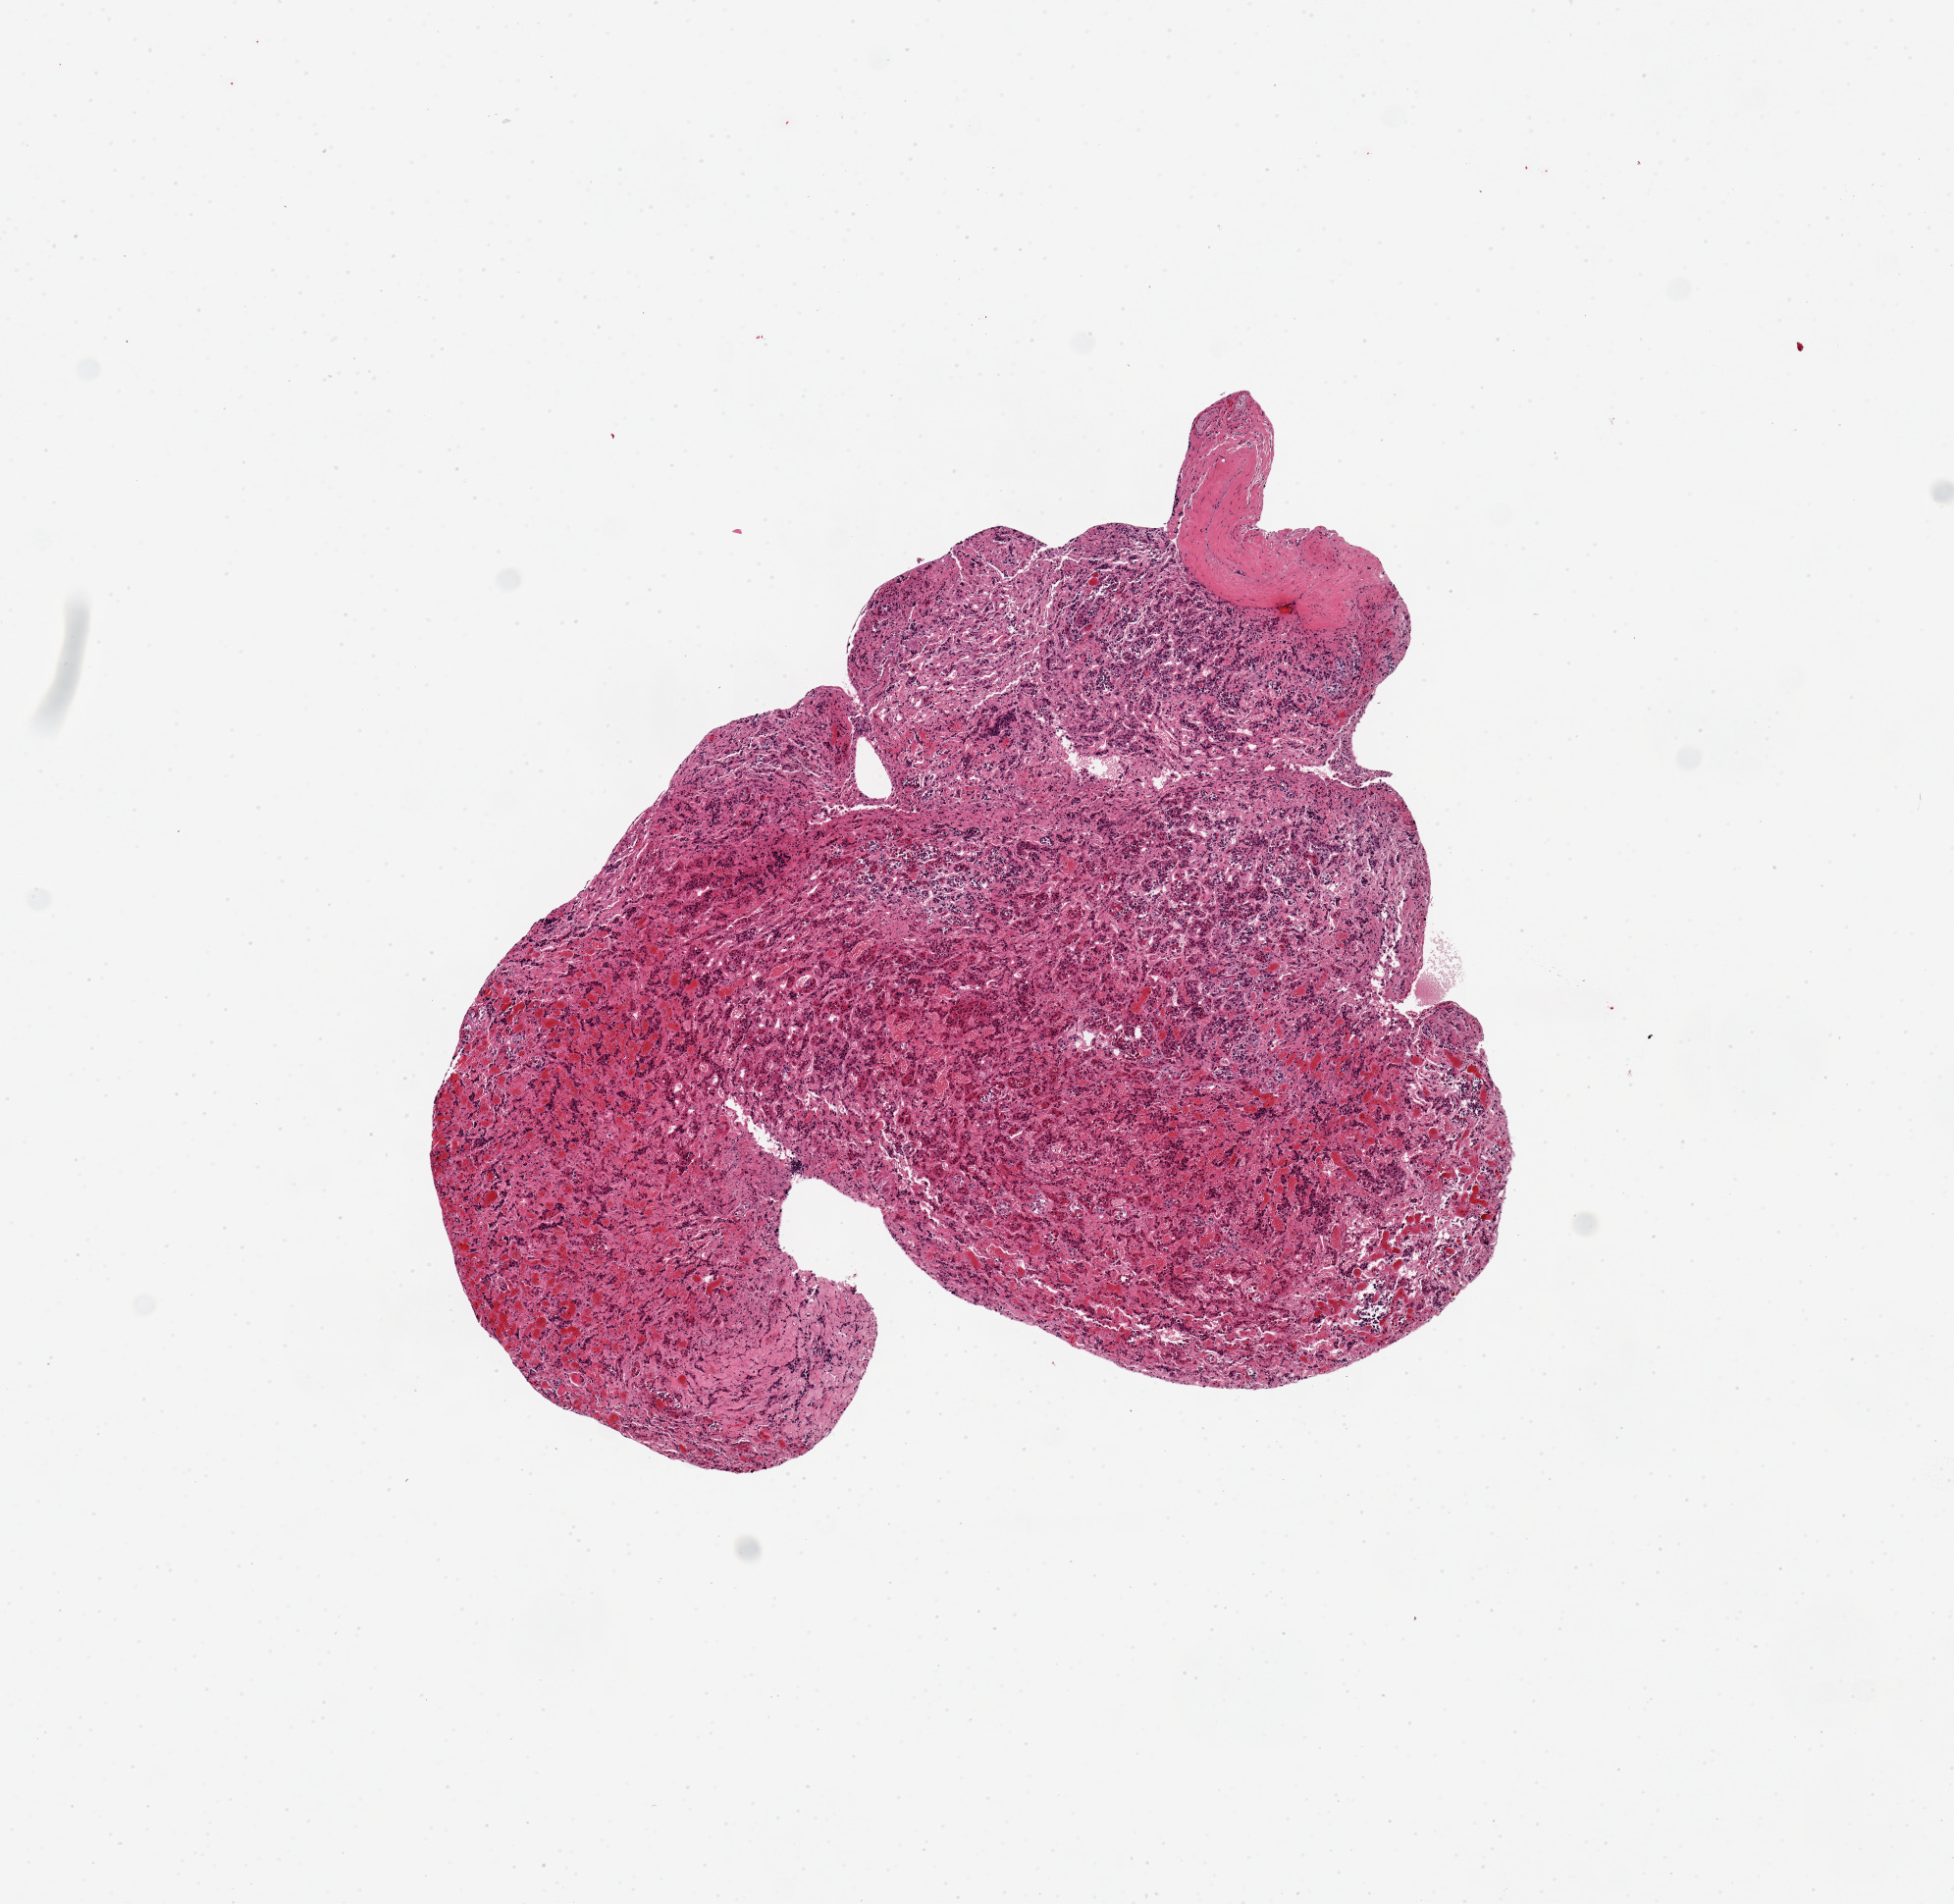
Haematoxylin and eosin whole-slide image, brightfield, shown as a low-resolution overview of the whole scanned area (about 7.9 x 7.7 mm, acquisition: 20x scan); PAXgene-fixed, paraffin-embedded tissue; sampled site (target tissue): pituitary; donor tissue sample. Donor: male.
Review note (as recorded): 1 pieces, moderately-severely autolyzed, all adenohypophysis.